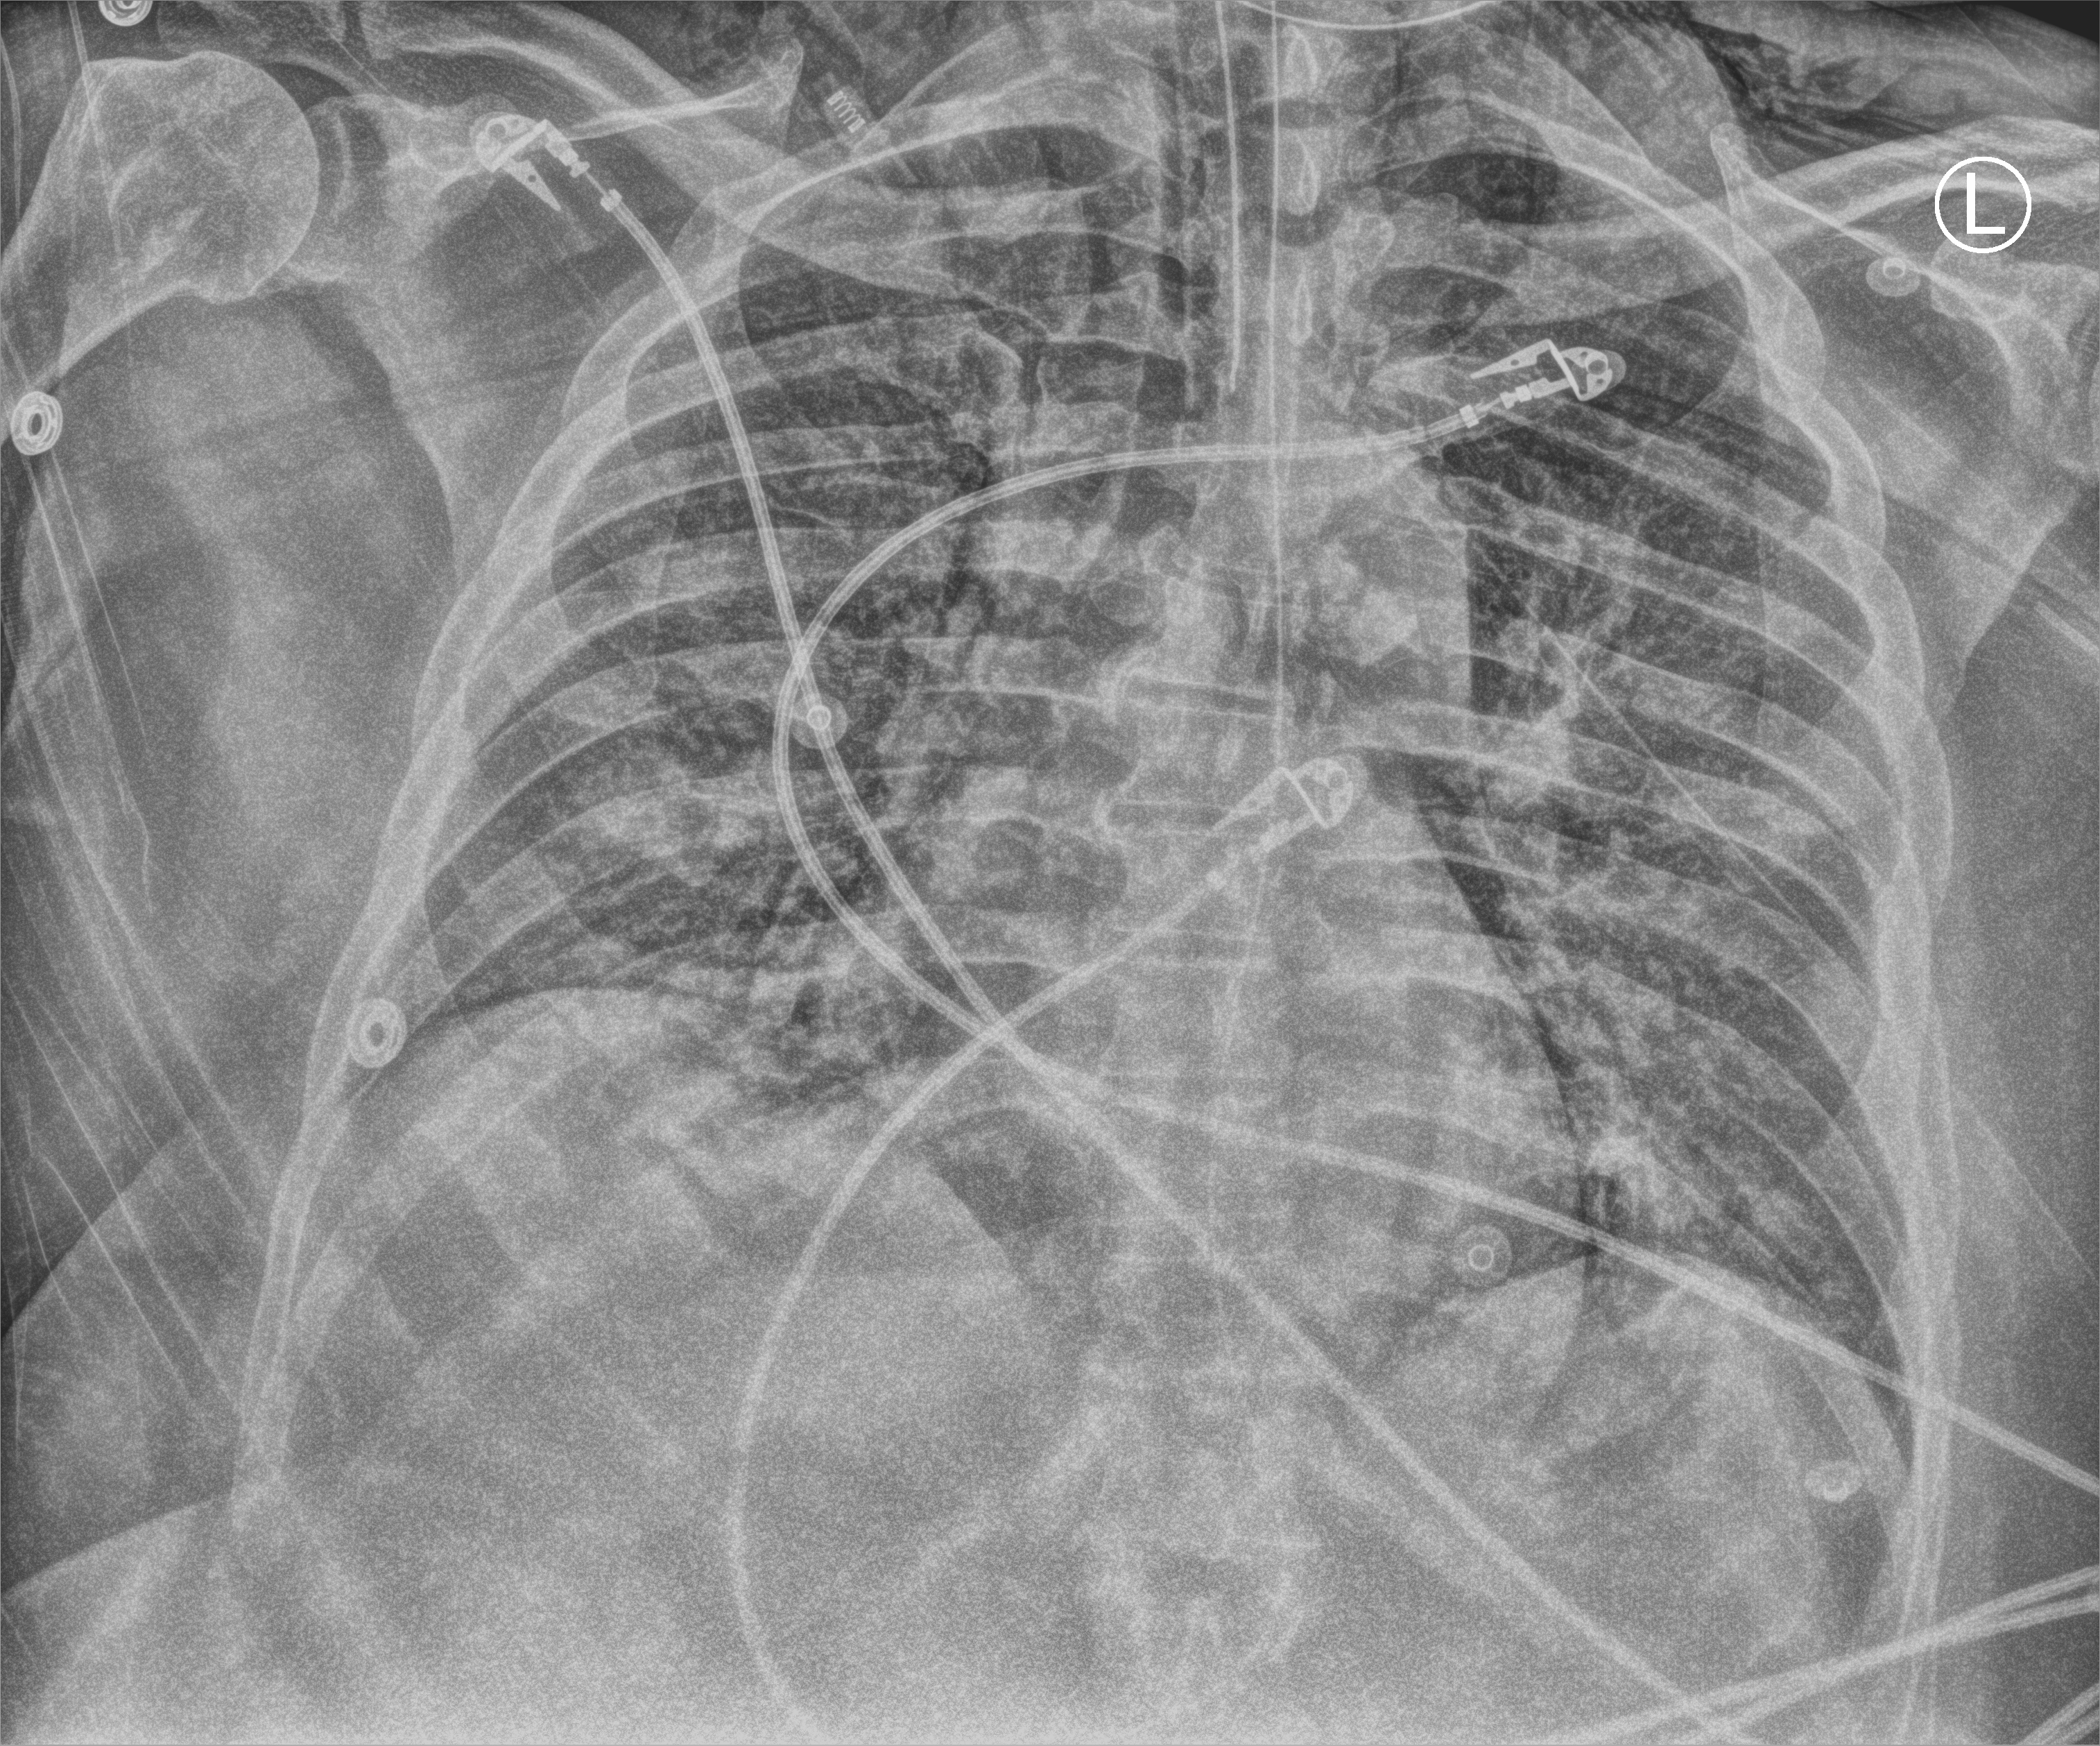
Bedside chest radiograph (computed radiography), anteroposterior (AP) projection. Patient hospitalised with COVID-19; male, aged 18–59 years.
Hospital-stay facts (about this admission, not read from this image; timing relative to this image not recorded):
- admitted to intensive care during this hospital stay: yes
- mechanically ventilated during this hospital stay: yes